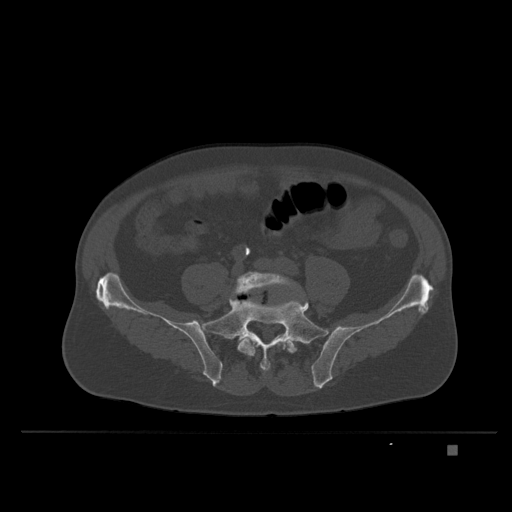
CT including the spine, one axial slice; slice 45 of 435 in the series (ordered by position); bone window (W 1800 / L 400 HU); 1.5 mm slice thickness; 512 × 512 image matrix, field of view 434 × 434 mm. Patient: male, 73 years. From the clinical record (not read from this slice): primary cancer: skin.
Annotated regions visible in this slice (semi-automatically segmented with operator editing):
- L5 vertebra: bounding box (x1, y1, x2, y2) in pixels: (233, 272, 301, 356)